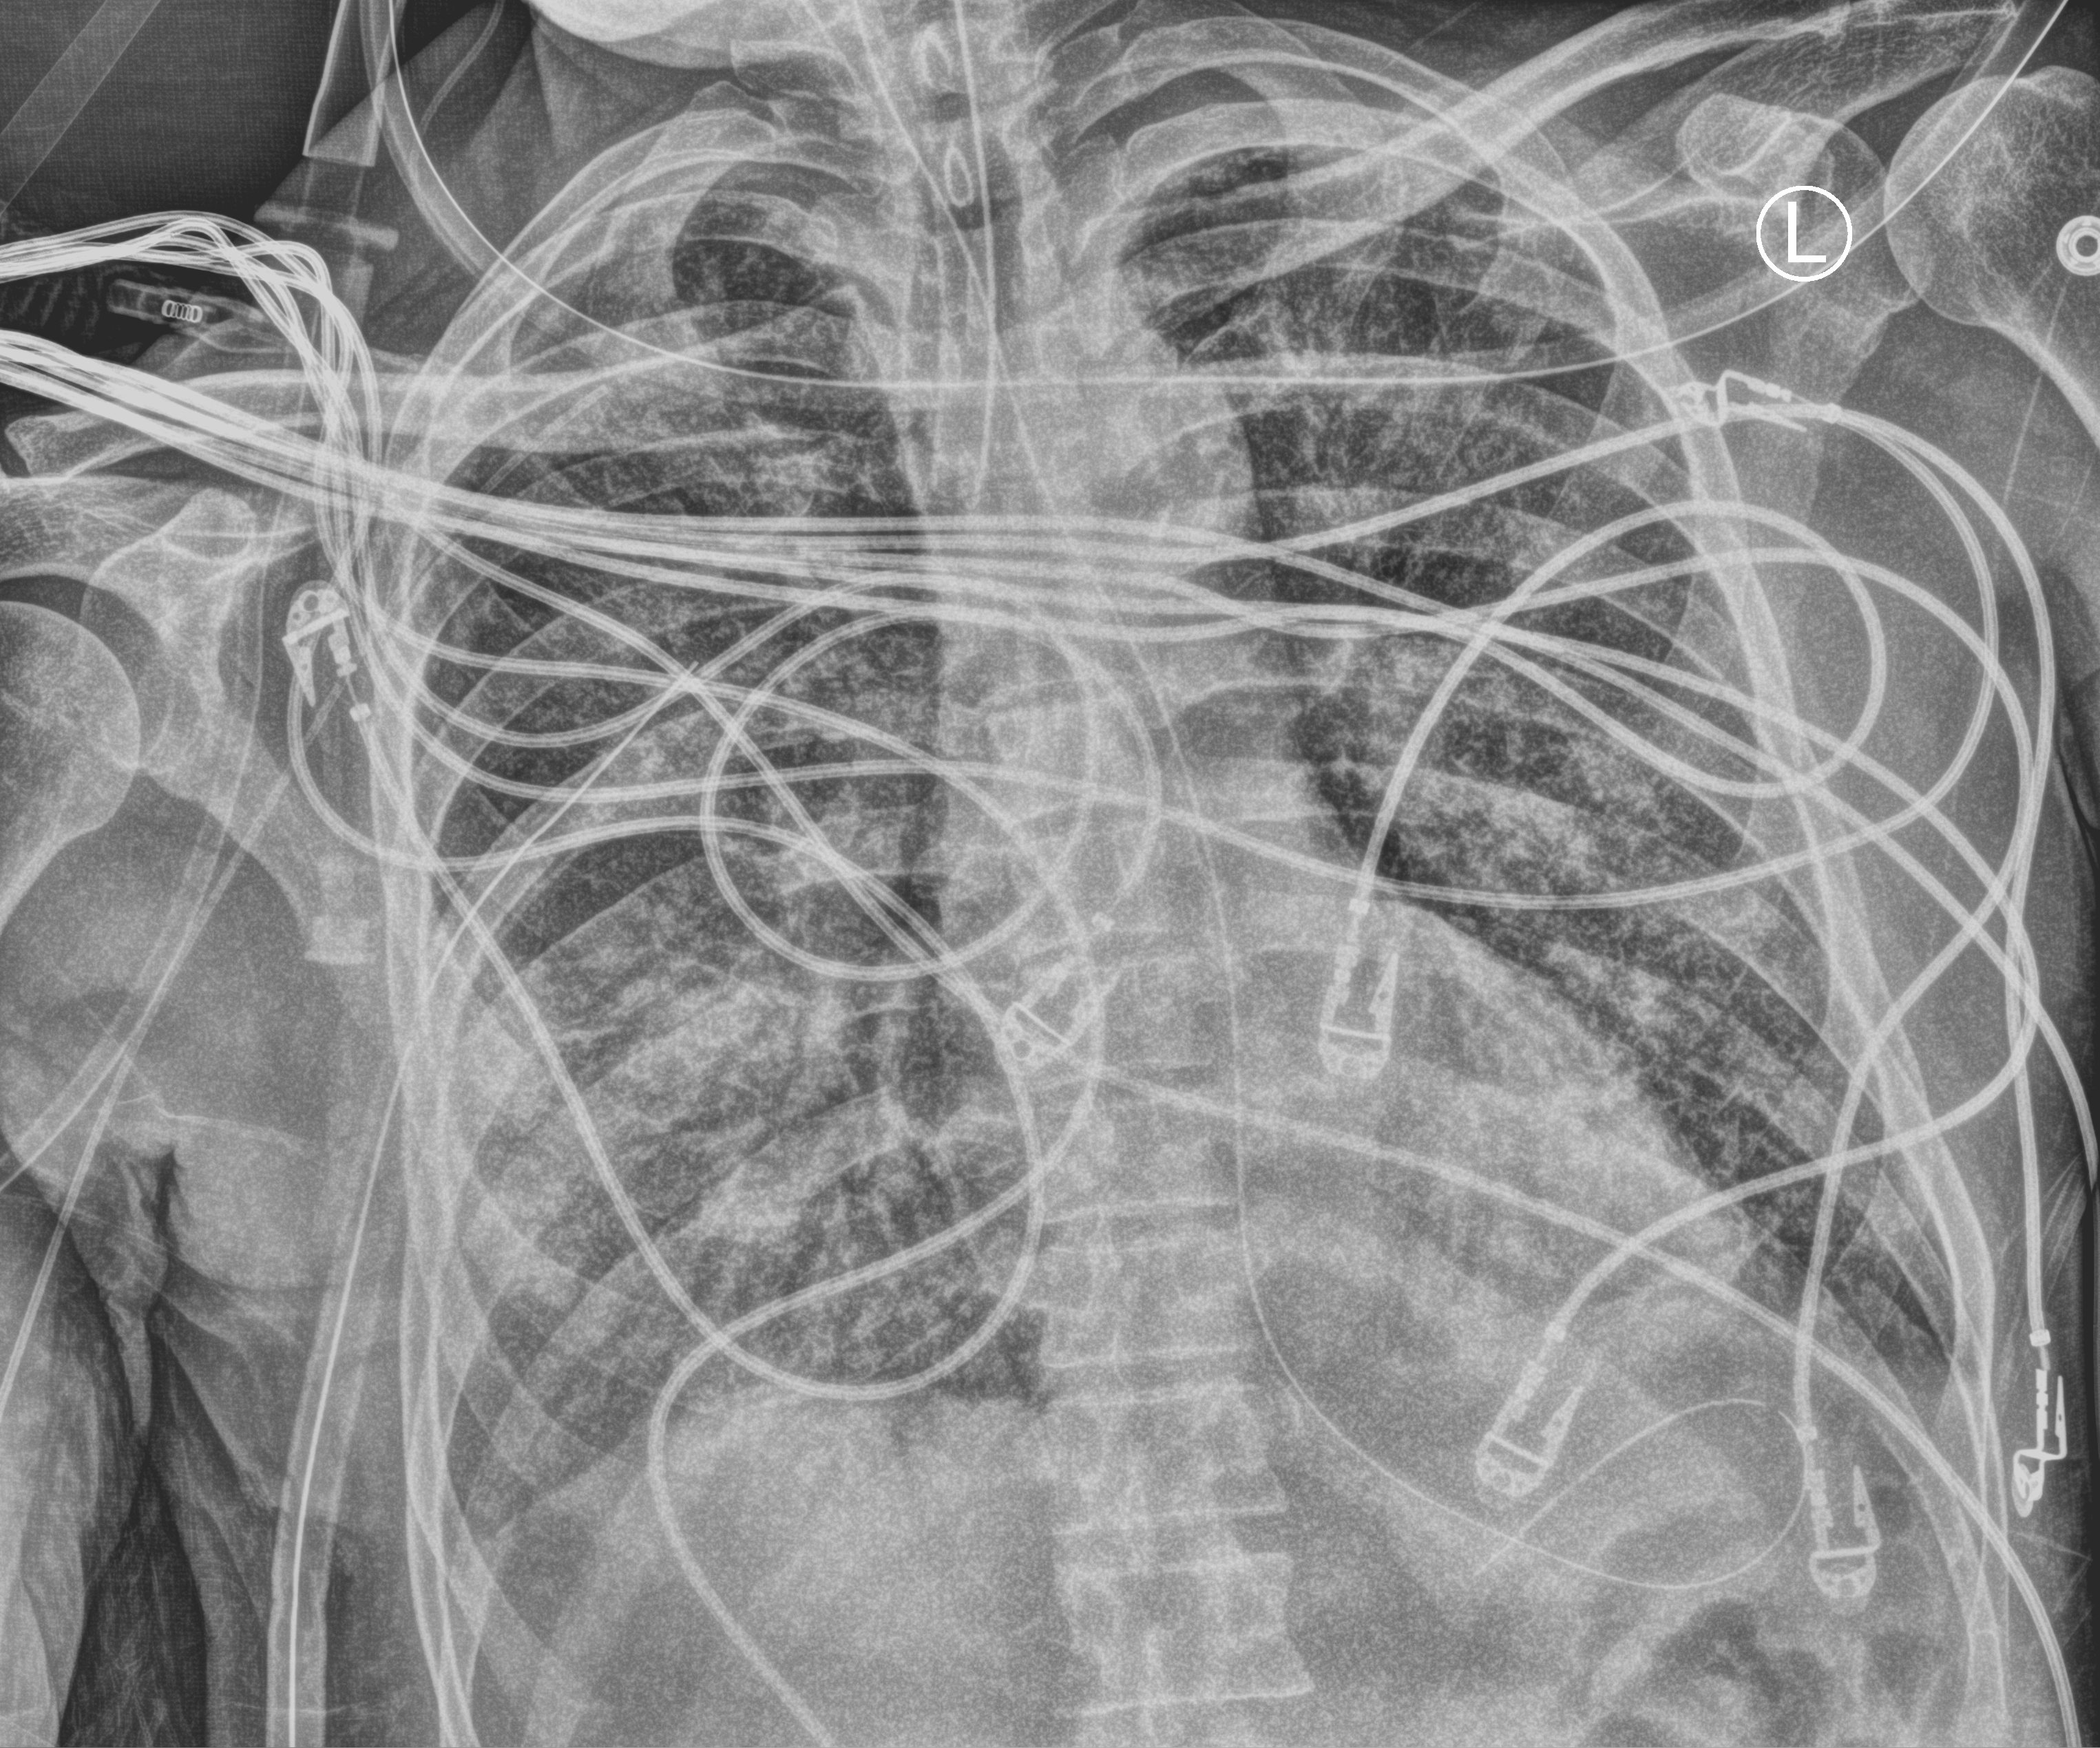
Portable chest radiograph, anteroposterior (AP) projection. Patient hospitalised with COVID-19; male, aged 60–74 years.
Hospital-stay facts (about this admission, not read from this image; timing relative to this image not recorded): mechanically ventilated during this hospital stay: yes; admitted to intensive care during this hospital stay: yes; length of hospital stay: 31 days.